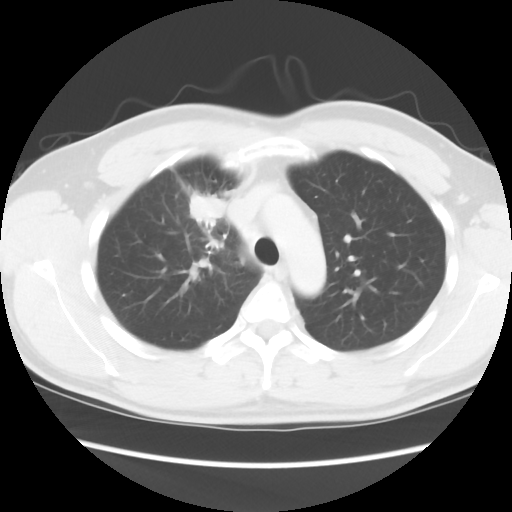
Chest CT, one axial slice; slice 65 of 80 in the series (ordered by position); reconstruction kernel STANDARD; lung window (W 1500 / L -600 HU); 5 mm slice thickness; 512 × 512 image matrix. Patient: male, 35 years. Case-level facts recorded for this patient, not image findings: clinical TNM (as recorded): T1c N1 M1b.
Annotated regions visible in this slice (bounding box drawn by a radiologist):
- lung tumour (recorded histology: adenocarcinoma): bounding box [x1, y1, x2, y2] px = [185, 189, 228, 226]